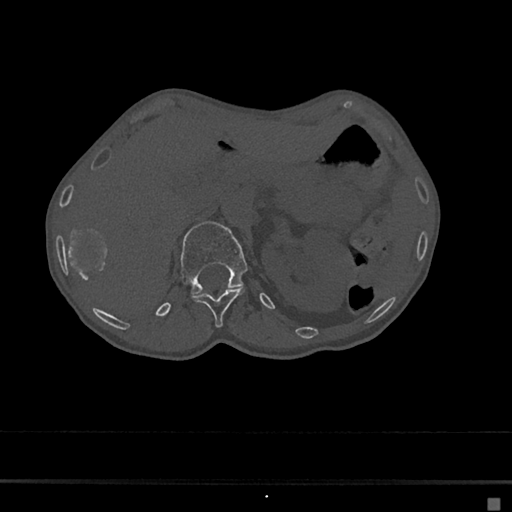
CT including the spine, one axial slice; position 93 of 797 along the scan axis; bone window (W 1800 / L 400 HU); 0.5 mm slice thickness; 512 × 512 image matrix, field of view 360 × 360 mm. Female patient, age 68 years. From the clinical record (not read from this slice): primary cancer: renal.
Outlined on this slice (semi-automatic segmentation, software-assisted and operator-edited):
- L1 vertebra: bounding box (x1, y1, x2, y2) in pixels: (180, 222, 248, 295)
- T12 vertebra: (192, 288, 244, 328)